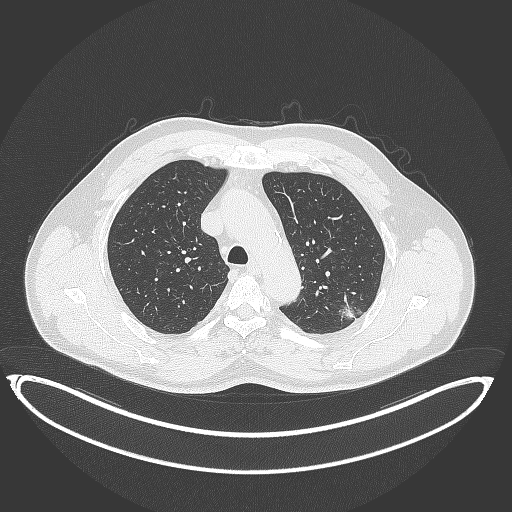
Chest CT, one axial slice. Slice 269 of 399 in the series (ordered by position). Reconstruction kernel B70f. Lung window (W 1500 / L -600 HU). 512 × 512 image matrix. Patient: male, 58 years. Case-level facts recorded for this patient, not image findings: clinical TNM (as recorded): T1c N0 M0; histopathological grade: G1-2.
Structures marked on this image (bounding box drawn by a radiologist):
- lung tumour (recorded histology: adenocarcinoma): bounding box [x1, y1, x2, y2] px = [338, 296, 363, 327]